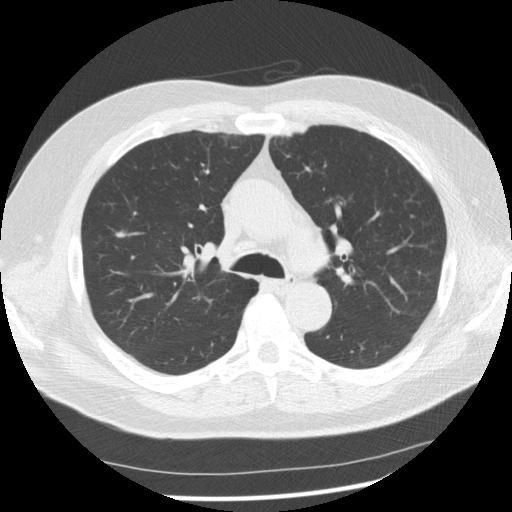
Axial slice from a low-dose chest CT screening exam; second screening round (one year after baseline); lung window (W 1500 / L -600 HU); 2.5 mm slice thickness; 120 kVp; slice 41 of 136 in the series. Male participant, aged 61 years at enrolment. Current smoker at enrolment.
Expert reader's lesion annotation, box from (x=97, y=218) to (x=141, y=255) px. Screening reader's record for this exam (one nodule recorded; not confirmed to be the boxed lesion): non-calcified nodule or mass ≥4 mm, right upper lobe, 7 × 7 mm, smooth margins, soft tissue attenuation, pre-existing on the prior screen: yes; interval growth: no. Official screen result: positive, no significant change: stable abnormalities potentially related to lung cancer, unchanged since the prior screening exam. Participant outcome: lung cancer diagnosed 389 days after this screen (after the third annual screen) — adenocarcinoma, NOS, right upper lobe, stage IIIA (AJCC 6th edition), 13 mm at pathology.